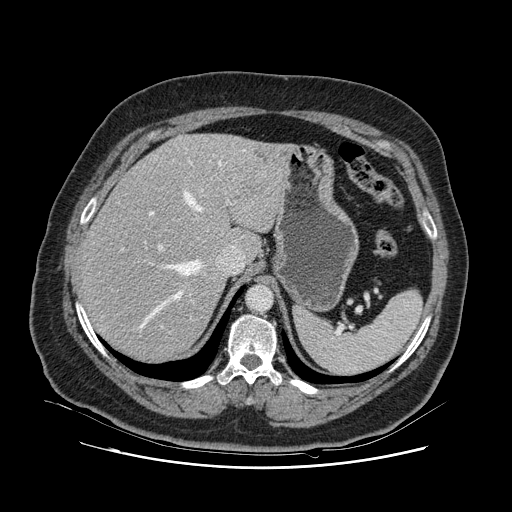
Contrast-enhanced abdominal CT, one axial slice. Position 86 of 132 along the scan axis. 120 kVp. Intravenous contrast given. Soft-tissue window (W 400 / L 40 HU). 2.5 mm slice thickness. 512 × 512 image matrix, field of view 391 × 391 mm. Female patient, age 73 years. From the clinical record (not read from this slice): diagnosis: colorectal cancer liver metastases, imaged before liver resection; multiple liver metastases: no; largest metastasis: 7 cm; chemotherapy before resection: yes.
Outlined on this slice (manually delineated by an expert):
- hepatic veins: box from (x=139, y=155) to (x=221, y=332) px
- liver: (x=82, y=134)–(x=288, y=362)
- planned liver remnant (the part of the liver to remain after resection): (x=82, y=161)–(x=245, y=362)
- portal vein (with intrahepatic branches): (x=121, y=161)–(x=192, y=328)